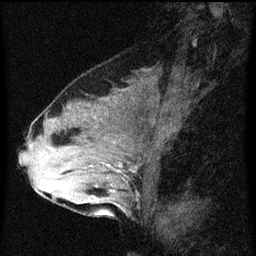
Breast MRI (dynamic contrast-enhanced), one sagittal slice; slice 28 of 60 in the series (ordered by position); dynamic contrast-enhanced series, image 2 of 3 at this slice position (ordered by acquisition); 1.5 T; TE 4.2 ms, TR 8 ms; 2 mm slice thickness; 256 × 256 image matrix, field of view 180 × 180 mm. Patient: female, 33 years.
Outlined on this slice (semi-automatic segmentation, software-assisted and operator-edited):
- analysis volume of interest (the breast-tissue region the enhancement analysis was run in; not a lesion): bounding box [x1, y1, x2, y2] px = [61, 126, 145, 213]
- tumour enhancement mask (voxels above the 70 % enhancement threshold inside the analysis volume of interest): [107, 164, 120, 167]